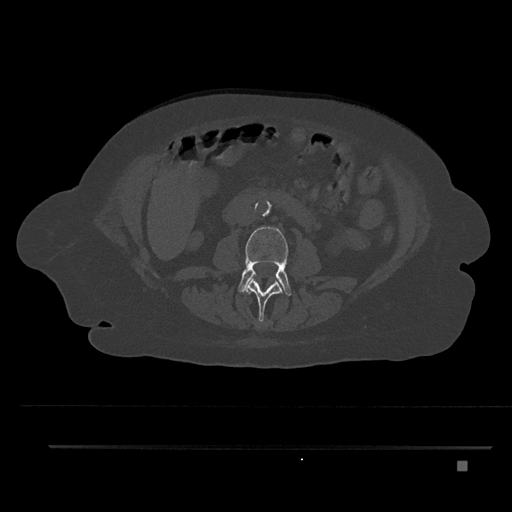
CT including the spine, one axial slice; position 149 of 797 along the scan axis; 120 kVp; bone window (W 1800 / L 400 HU); 0.5 mm slice thickness; 512 × 512 image matrix, field of view 437 × 437 mm. Patient: female, 76 years. Case-level facts recorded for this patient, not image findings: primary cancer: lung; vertebrae with lytic lesions (as recorded): T11, L3.
Annotated regions visible in this slice (semi-automatically segmented with operator editing):
- L2 vertebra: bounding box (x1, y1, x2, y2) in pixels: (245, 279, 283, 323)
- L3 vertebra: (238, 227, 292, 296)